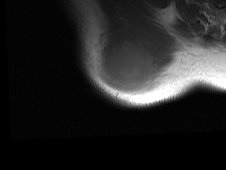
MRI of an extremity soft-tissue mass, one axial slice. Slice 58 of 81 in the series (ordered by position). MR volume resampled by the dataset authors to the PET/CT grid (not the native acquisition matrix). 3.27 mm slice thickness. 226 × 170 image matrix. Male patient. Case-level facts recorded for this patient, not image findings: histological type: pleiomorphic spindle cell undifferentiated; grade: high; site of the primary tumour: right parascapusular.
Structures marked on this image (expert contour drawn on MRI and transferred to this co-registered scan by the dataset authors):
- gross tumour volume including surrounding oedema: box from (x=97, y=36) to (x=182, y=98) px
- gross tumour volume (mass): (x=101, y=43)–(x=155, y=94)